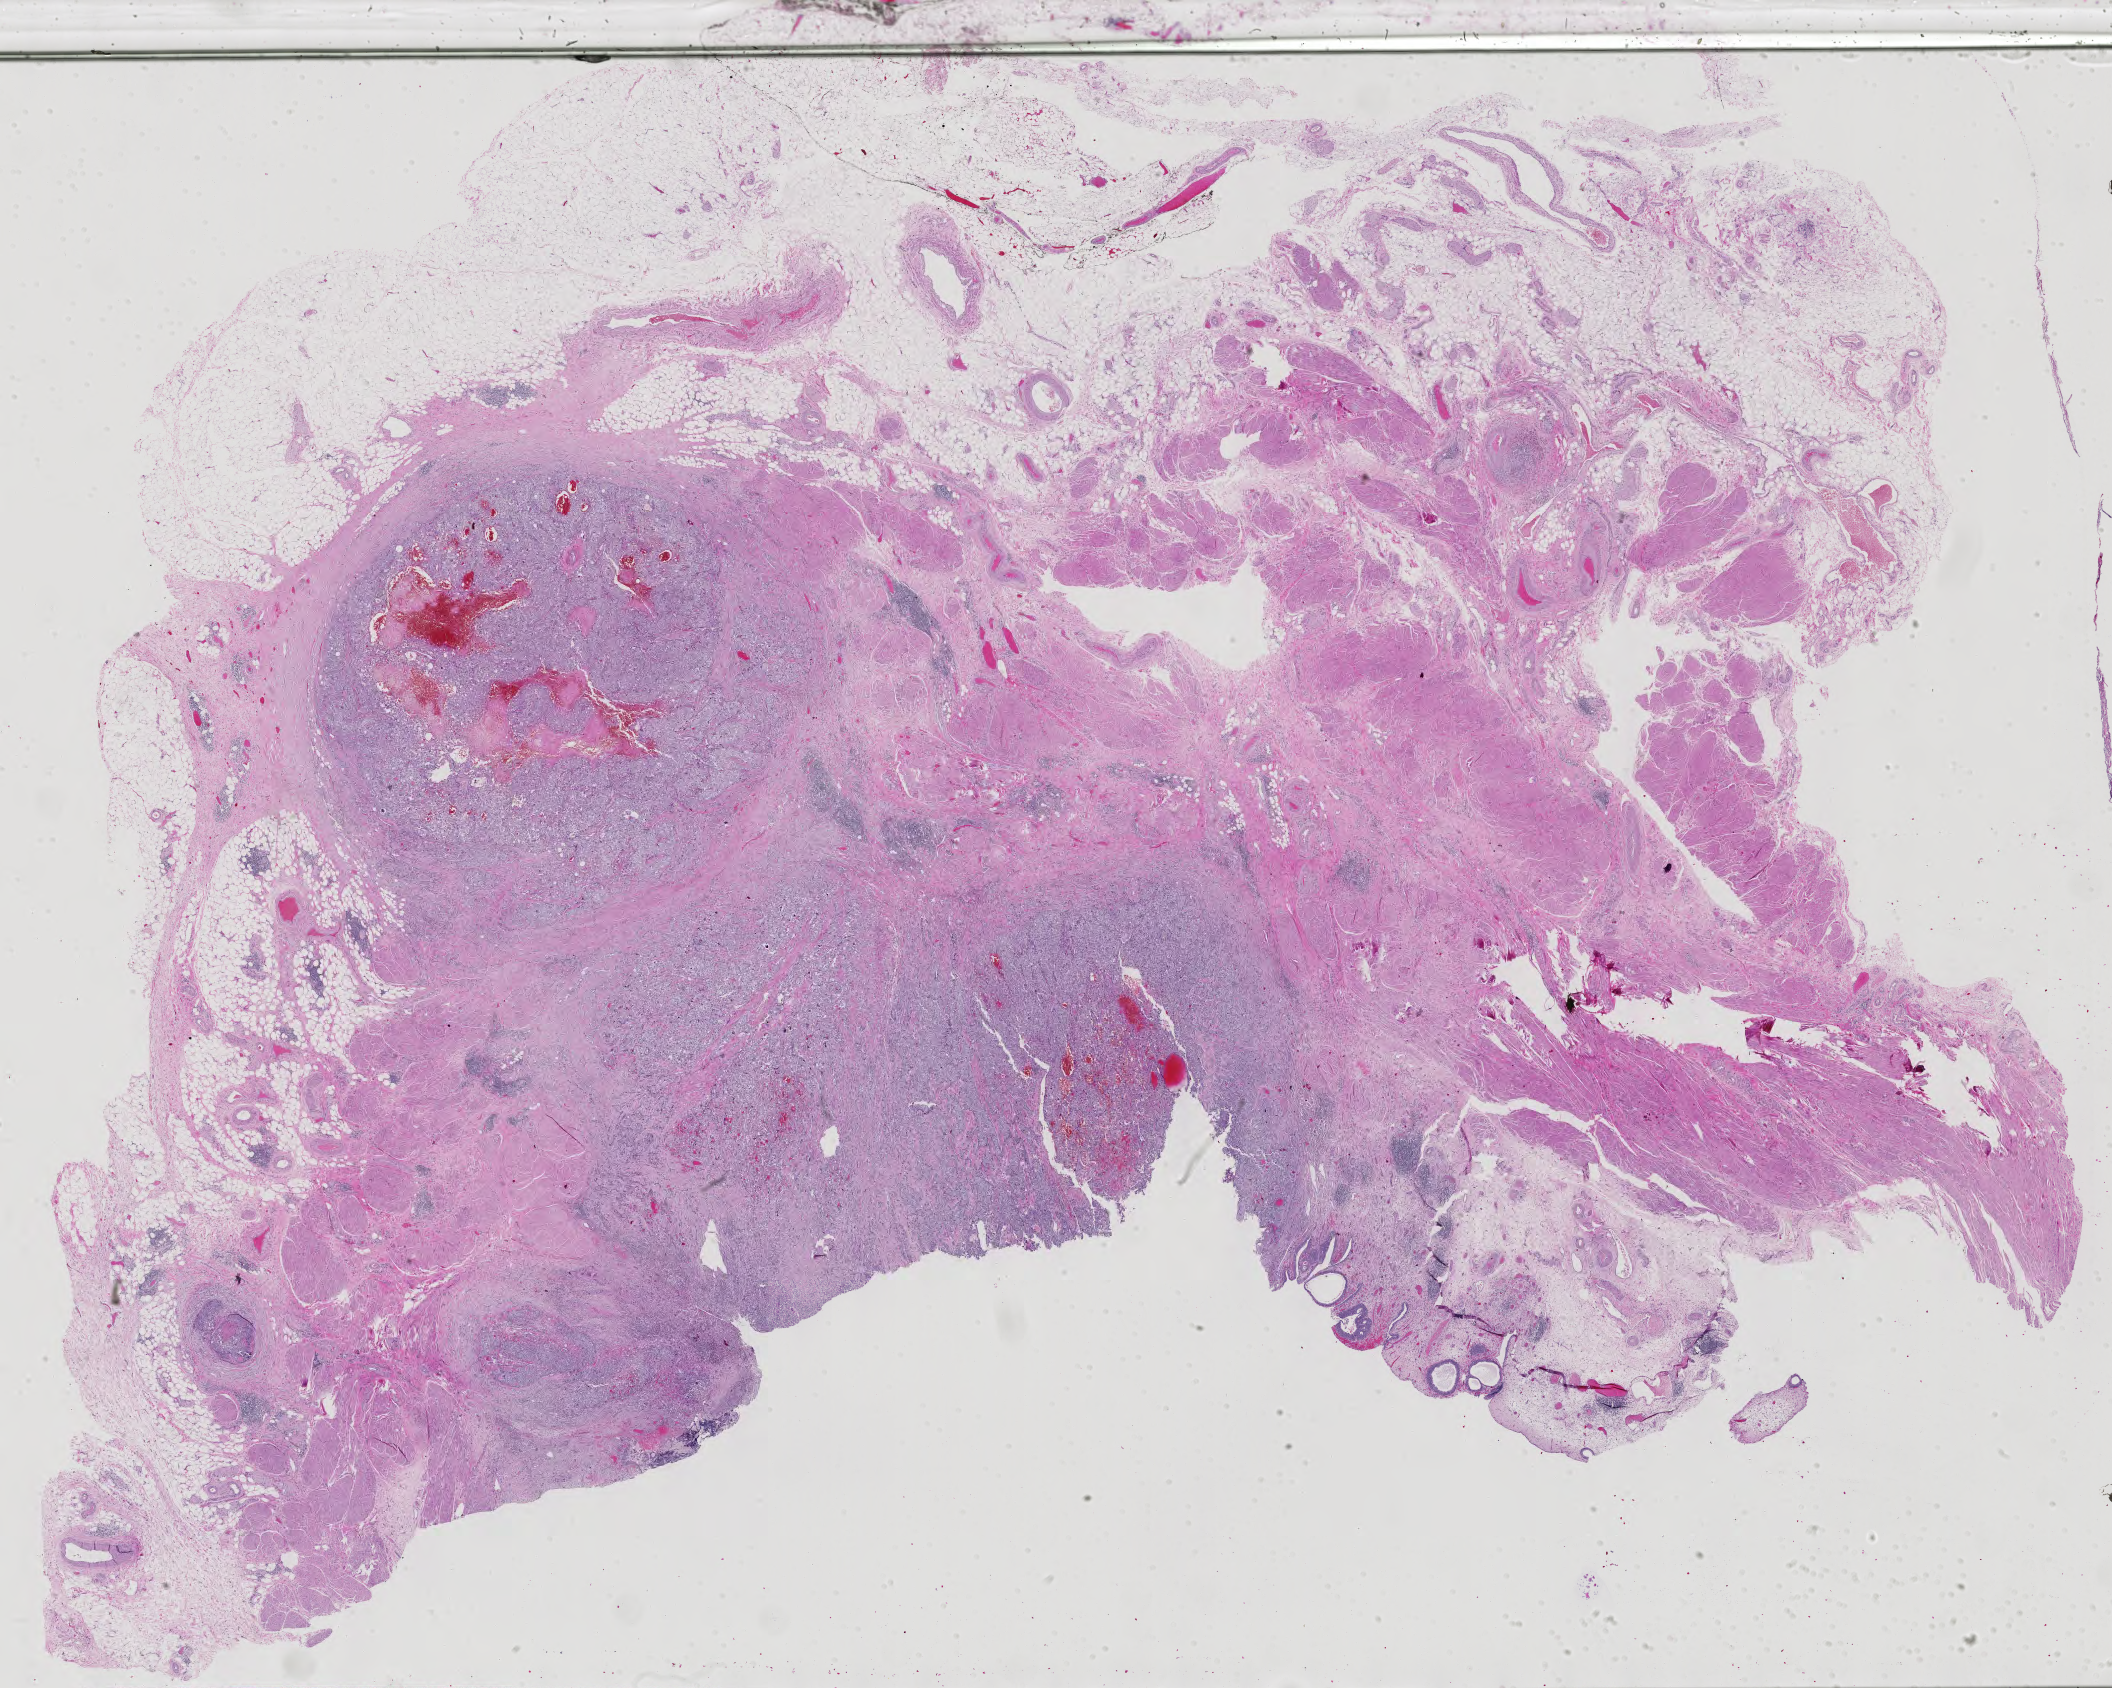
Whole-slide histology image, Hematoxylin and eosin (H&E) stained — low-resolution overview of the scanned area, about 30.8 x 24.6 mm (from a 40x scan). Formalin-fixed paraffin-embedded (FFPE) diagnostic section. Sample: primary tumour, bladder. Female patient; age at initial diagnosis 67 years. Histologic grade: high grade.
Lymph nodes positive (case pathology): 0 of 16 examined. AJCC pathologic stage: III (7th edition). Pathologic diagnosis: Transitional cell carcinoma.